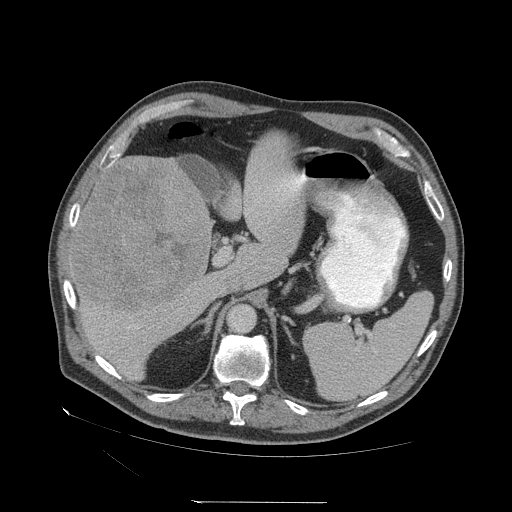
Contrast-enhanced abdominal CT (liver protocol), one axial slice. Reconstruction kernel STANDARD. 140 kVp. Soft-tissue window (W 400 / L 40 HU). 2.5 mm slice thickness. 512 × 512 image matrix, field of view 460 × 460 mm. From the clinical record (not read from this slice): diagnosis: hepatocellular carcinoma (patient treated with transarterial chemoembolisation; whether this scan precedes or follows treatment is not stated here); TNM stage (as recorded): Stage-I.
Structures marked on this image (semi-automatic segmentation, software-assisted and operator-edited):
- liver parenchyma outside the tumour (the mass and vessels are separate outlines, so this box may not span the whole liver): box from (x=68, y=156) to (x=276, y=380) px
- mass: (x=72, y=155)–(x=211, y=310)